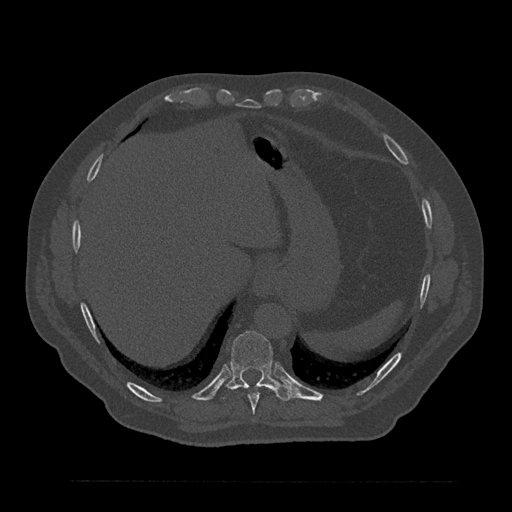
CT including the spine, one axial slice; position 371 of 797 along the scan axis; 120 kVp; bone window (W 1800 / L 400 HU); 512 × 512 image matrix. Patient: male, 61 years. Case-level facts recorded for this patient, not image findings: primary cancer: prostate.
Structures marked on this image (semi-automatically segmented with operator editing):
- T10 vertebra: box from (x=222, y=331) to (x=293, y=401) px
- T9 vertebra: (x=248, y=384)–(x=266, y=414)